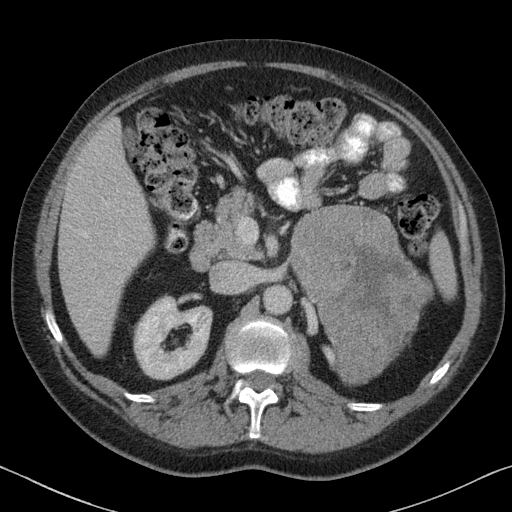
Contrast-enhanced abdominal CT, one axial slice. Slice 43 of 88 in the series (ordered by position). Reconstruction kernel B31f. Intravenous contrast given. Soft-tissue window (W 400 / L 40 HU). 3 mm slice thickness. 512 × 512 image matrix, field of view 366 × 366 mm. Patient: male, 51 years. From the clinical record (not read from this slice): diagnosis: adrenocortical carcinoma; tumour side: left adrenal; tumour size at pathology: 16.5 cm; Ki-67 index: 30 %; stage (as recorded): 2.
Outlined on this slice (semi-automatic segmentation, software-assisted and operator-edited):
- mass: bounding box (x1, y1, x2, y2) in pixels: (292, 205, 430, 385)